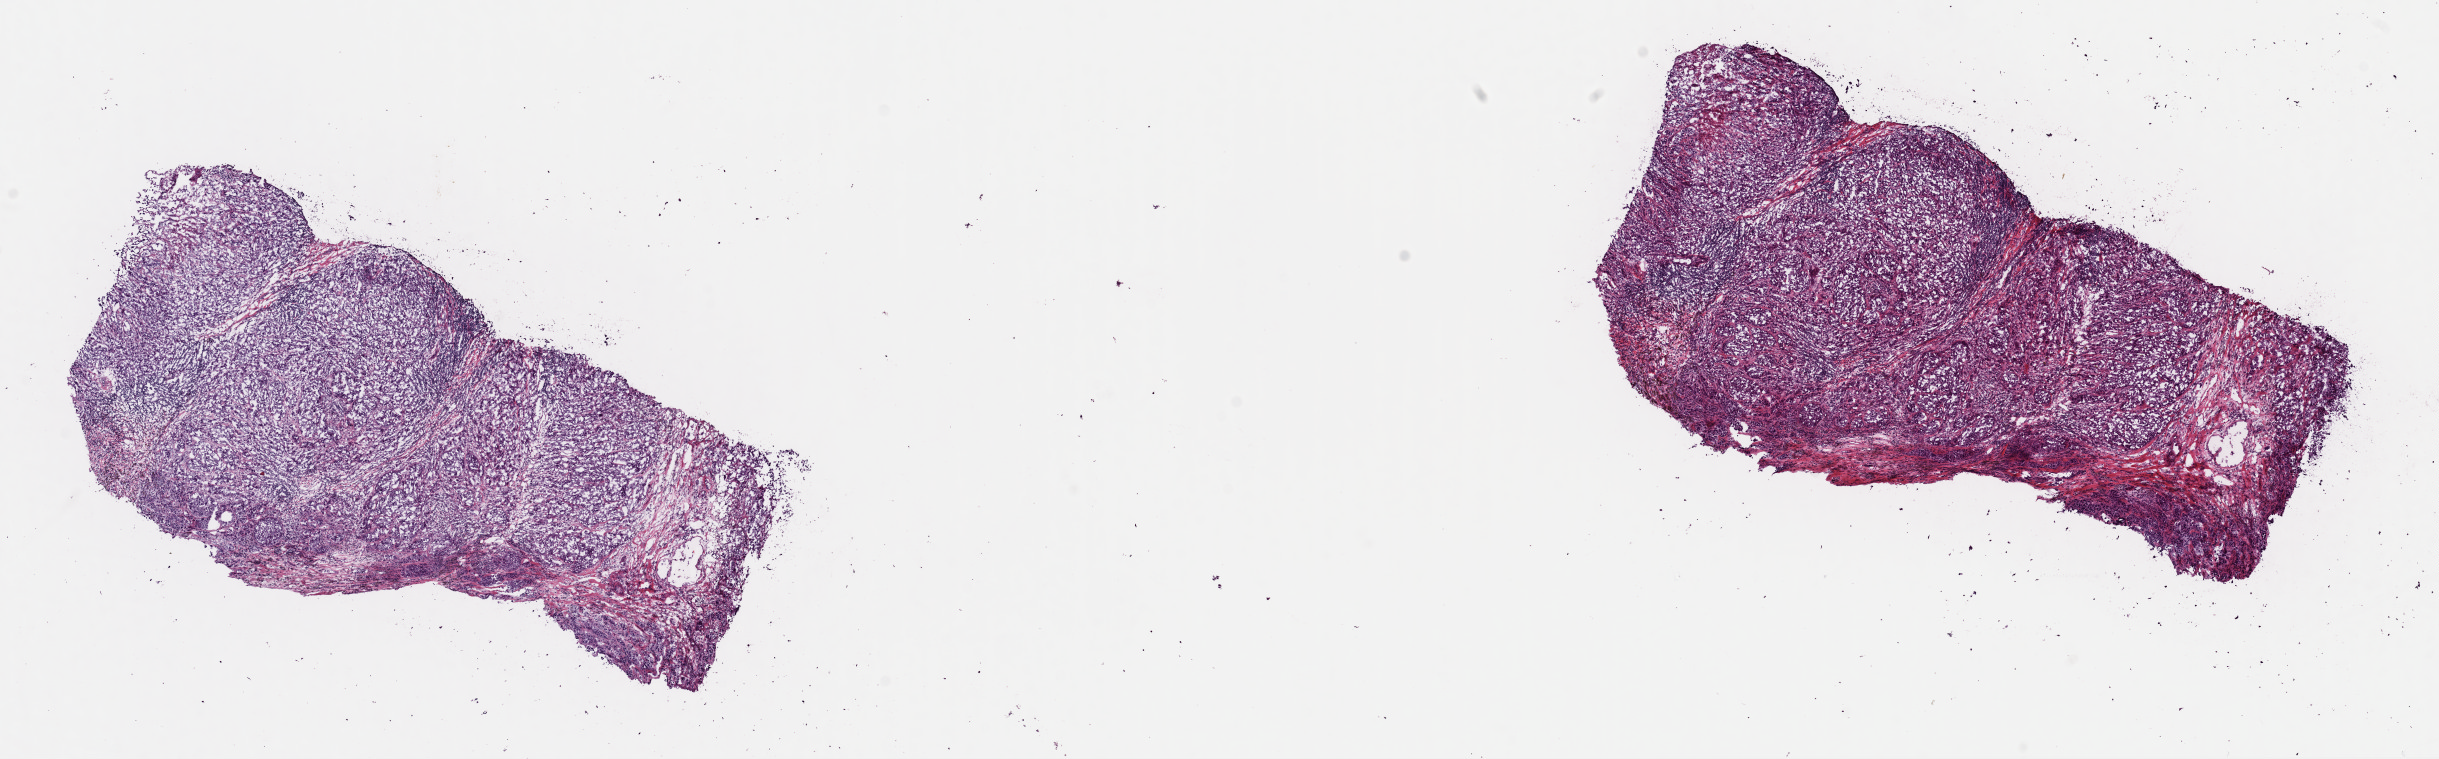
Digitized Hematoxylin and eosin (H&E) stained tissue section (whole slide), low-resolution overview of the scanned area, about 19.3 x 6.0 mm (from a 40x scan). Frozen section. Metastatic tumour sample, sampled site not recorded. Male patient; age at initial diagnosis 78 years. Pathologist review of this section (percent, as recorded): tumour cells 75%, tumour nuclei 75%, normal cells 0%, stromal cells 25%, necrosis 0%. Infiltration values recorded for this section: lymphocyte infiltration 10%, monocyte infiltration 0%, neutrophil infiltration 0%.
This section: metastatic tumour tissue. Patient diagnosis: Malignant melanoma, NOS.